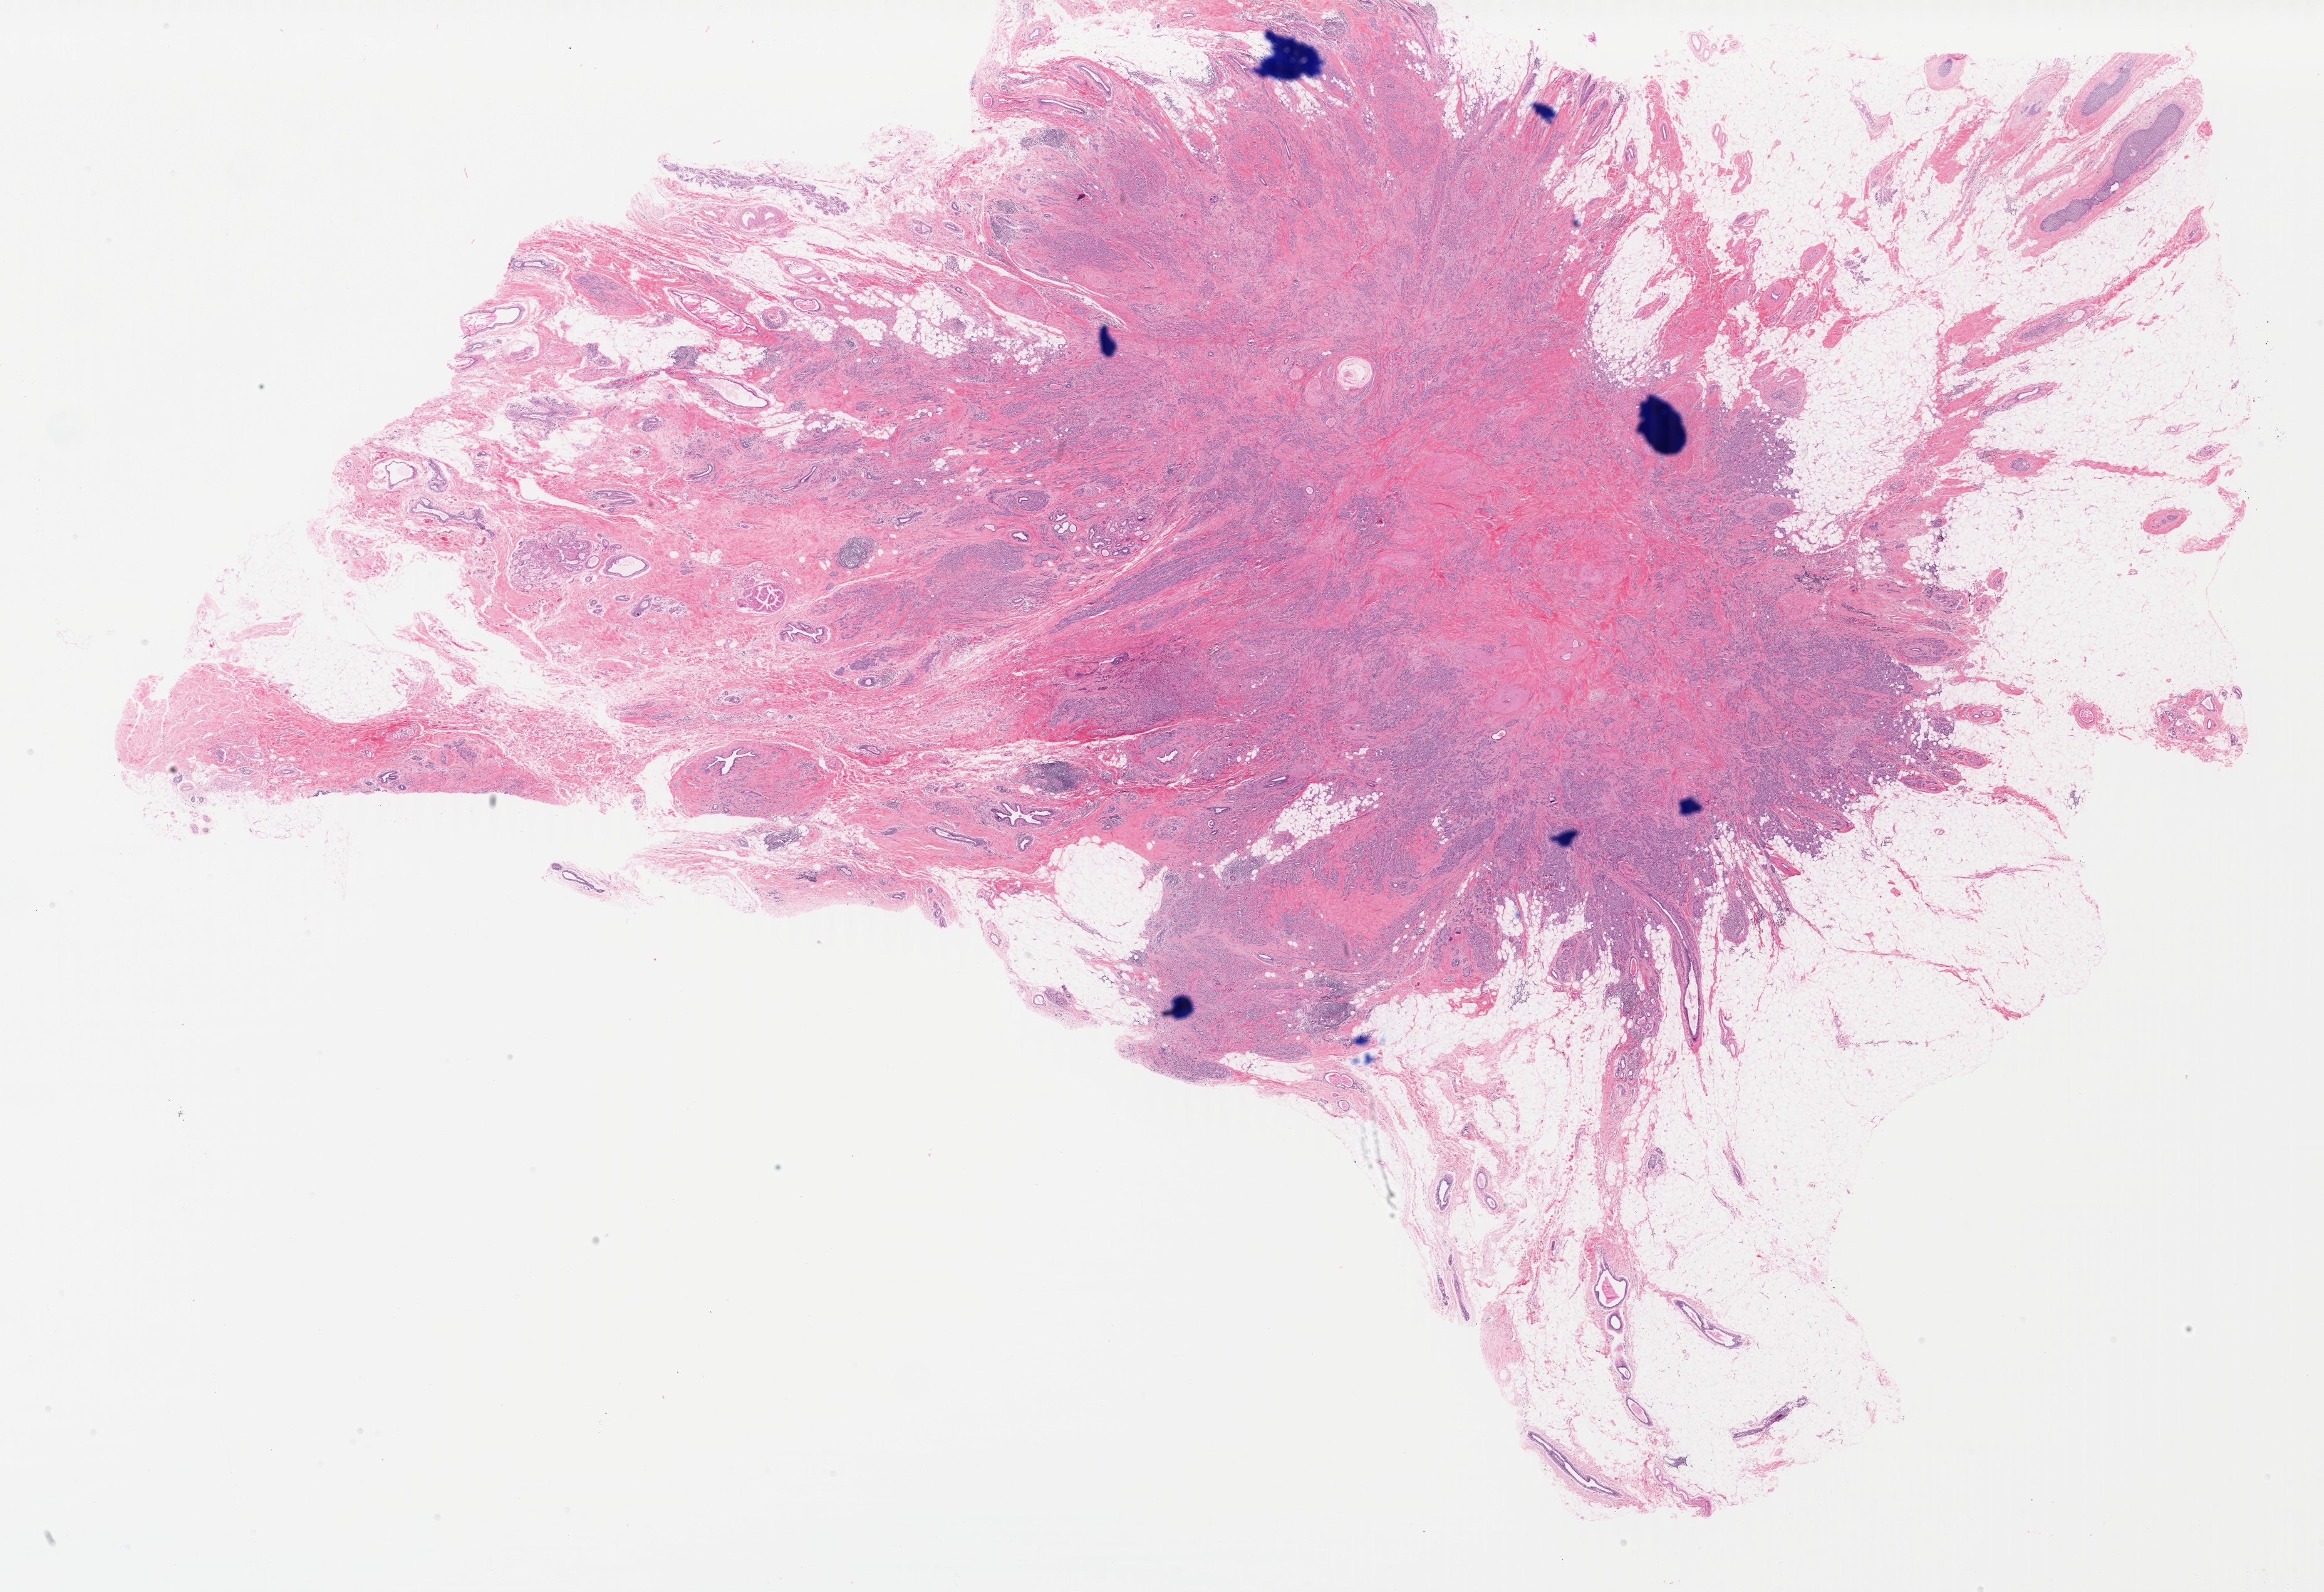
Whole-slide histology image, H&E — low-resolution overview of the scanned area, about 29.5 x 20.2 mm (acquisition: 40x scan), FFPE section, primary tumour sample from the breast. Female patient; age at initial diagnosis 74 years.
Diagnosis: Lobular carcinoma, NOS.